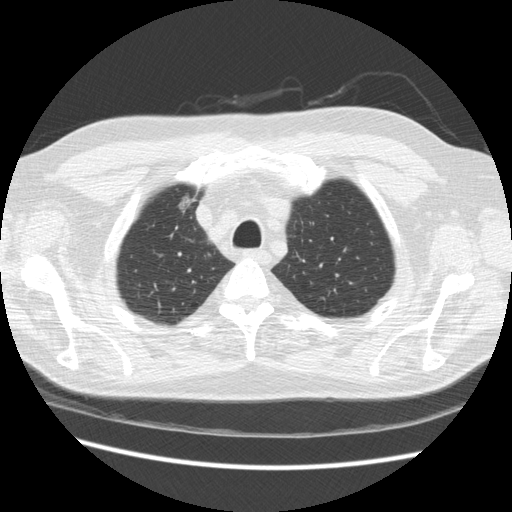
Chest CT (low-dose screening protocol), one axial image. Third annual screen. Lung window (W 1500 / L -600 HU). Standard (soft-tissue) reconstruction kernel (STANDARD). Slice 43 of 234 in the series. Male participant, aged 66 years at enrolment. Former smoker at enrolment.
Expert-annotated lung lesion, box from (x=167, y=185) to (x=208, y=221) px. Screening reader's record for this exam: no non-calcified nodule ≥4 mm recorded. Lung cancer was diagnosed 229 days after this screen: bronchiolo-alveolar adenocarcinoma, NOS, right upper lobe, moderately differentiated (G2), stage IA (AJCC 6th edition), 12 mm at pathology.